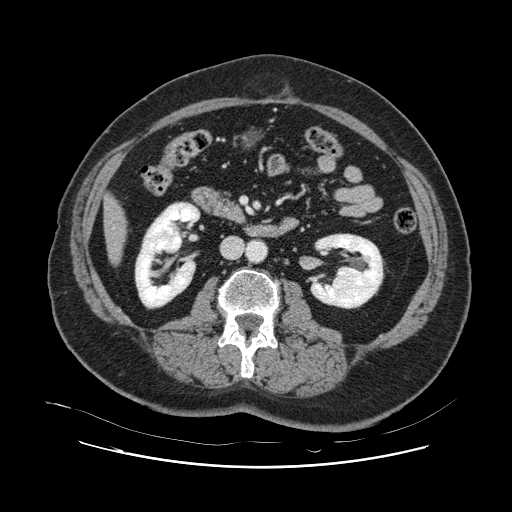
Contrast-enhanced abdominal CT, one axial slice; slice 23 of 132 in the series (ordered by position); intravenous contrast given; soft-tissue window (W 400 / L 40 HU); 512 × 512 image matrix, field of view 391 × 391 mm. Female patient, age 73 years. From the clinical record (not read from this slice): diagnosis: colorectal cancer liver metastases, imaged before liver resection; multiple liver metastases: no; largest metastasis: 7 cm.
Structures marked on this image (expert manual segmentation):
- liver: bounding box <105,198,125,262> (left, top, right, bottom; pixels)
- planned liver remnant (the part of the liver to remain after resection): <105,198,125,261>